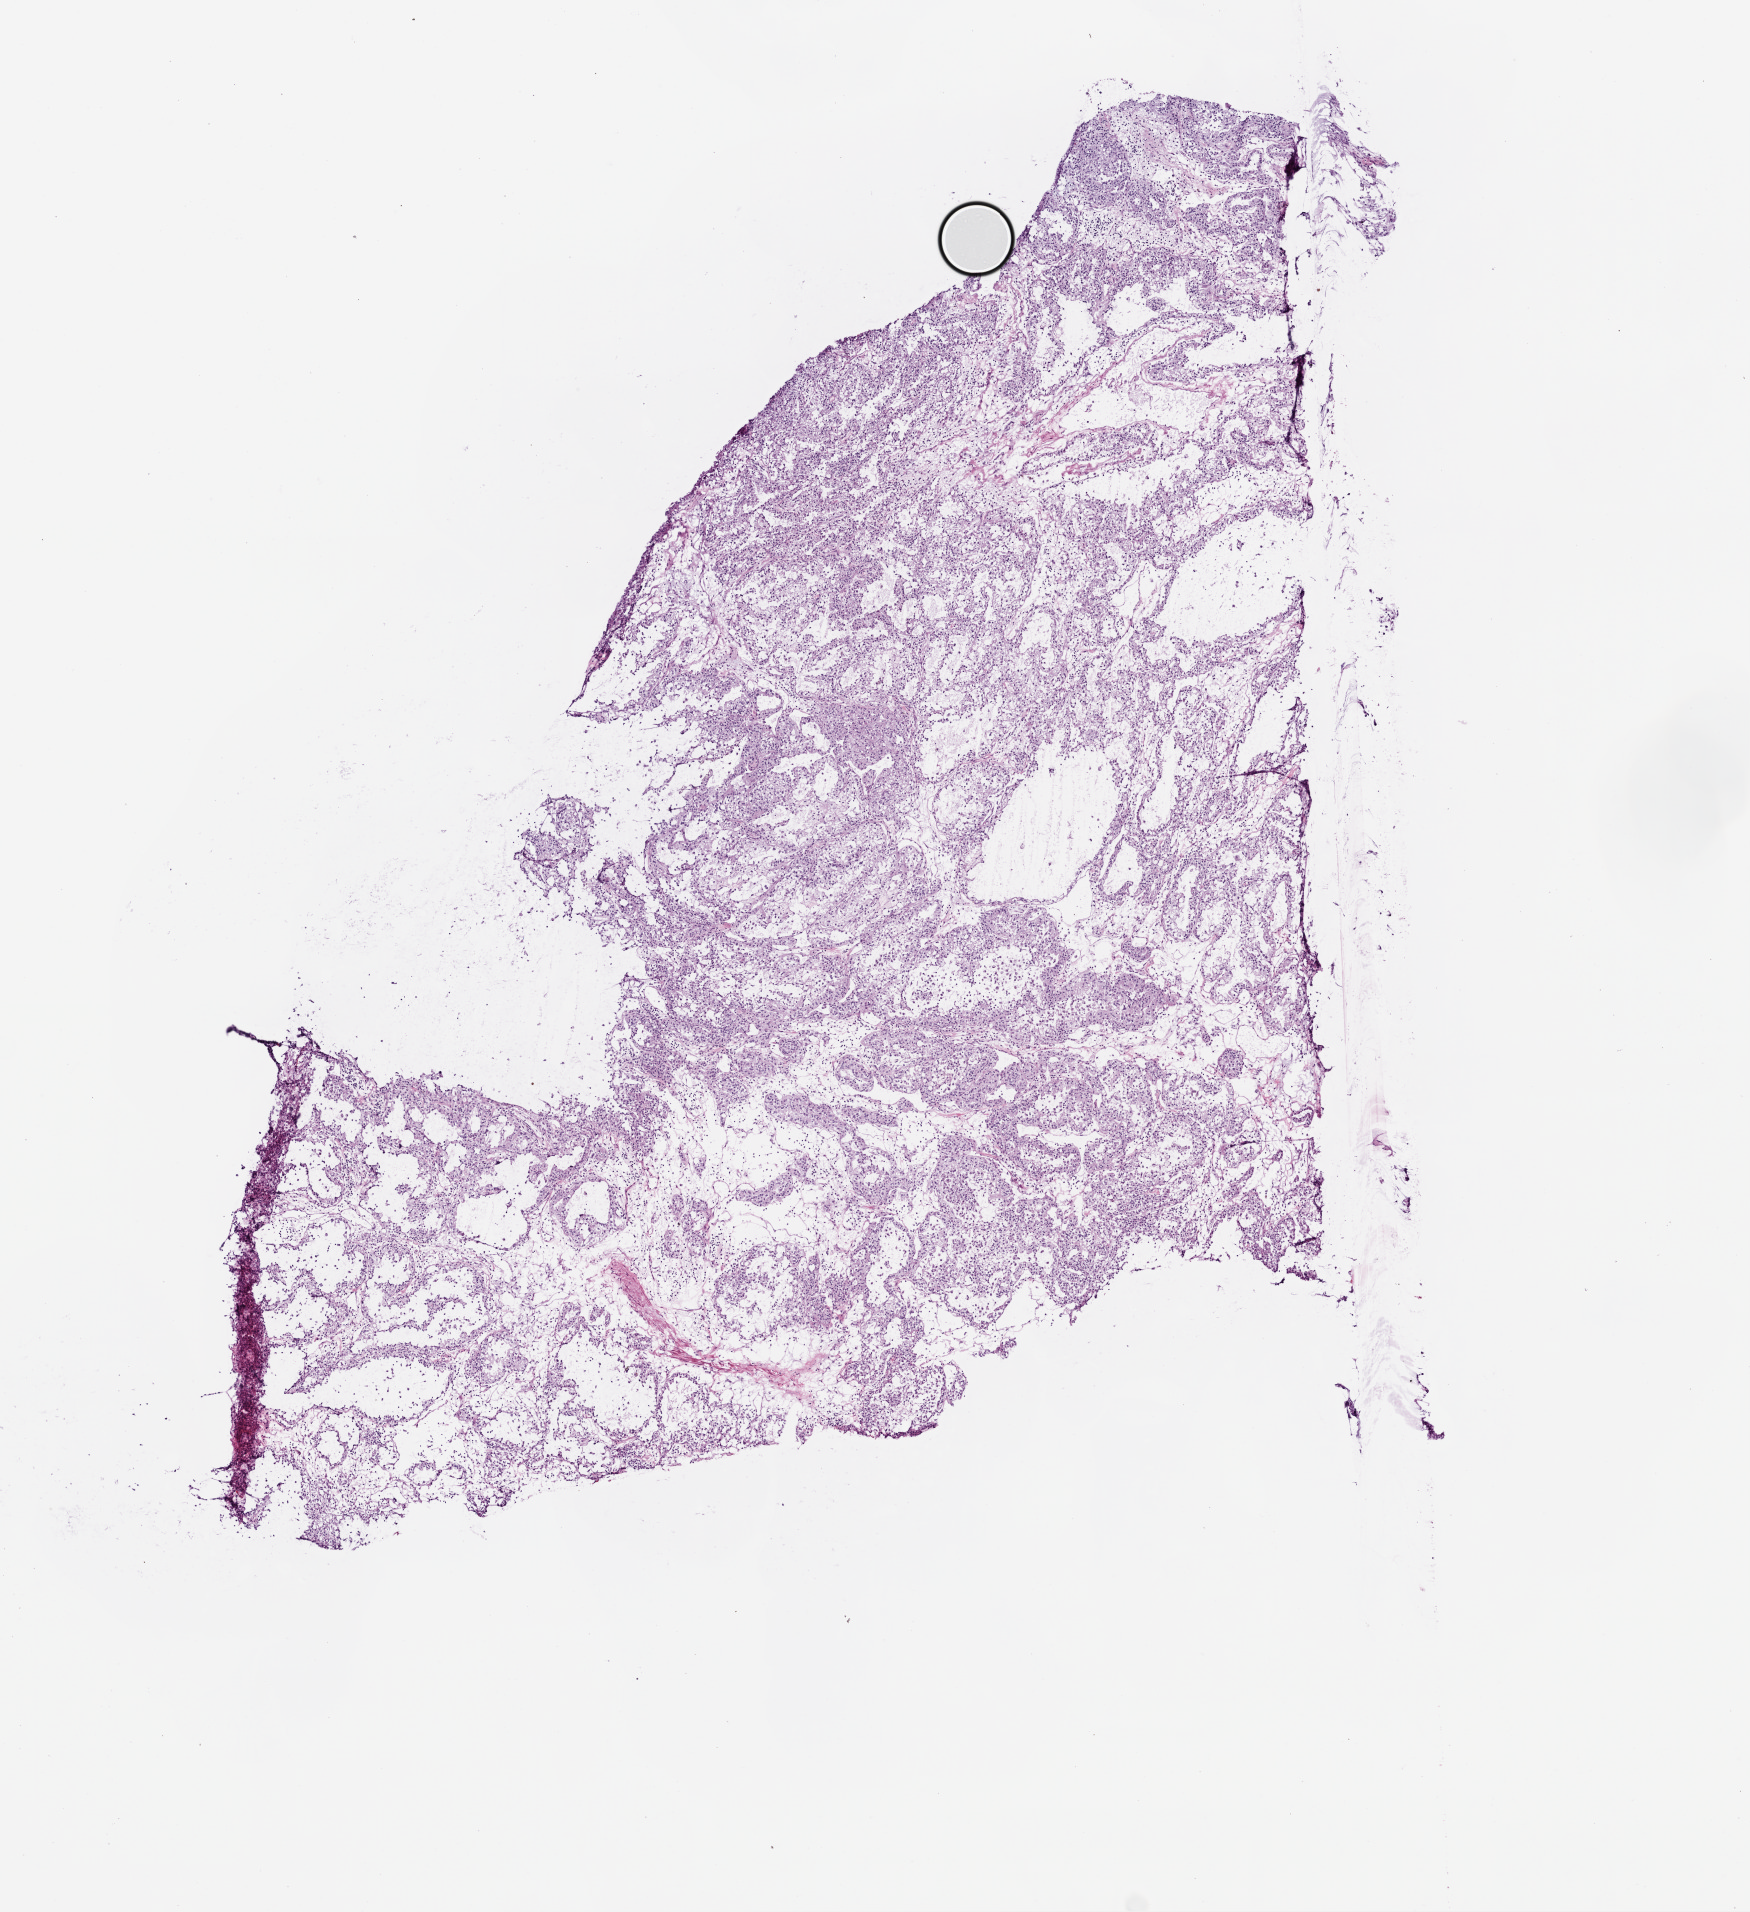
Digitized H&E tissue section (whole slide), shown as a low-resolution overview of the whole scanned area (about 7.0 x 7.7 mm, acquisition: 20x scan). Frozen section from the top of the tissue portion. Primary tumour sample from the kidney. Male, age 65 years at initial diagnosis. Histologic grade: G3 (poorly differentiated). Slide review estimates, as recorded: tumour cells 90%, tumour nuclei 80%, normal cells 0%, stromal cells 10%, necrosis 0%.
- TNM: T3a N0 M0
- diagnosis: Clear cell adenocarcinoma, NOS
- AJCC pathologic stage: III (7th edition)